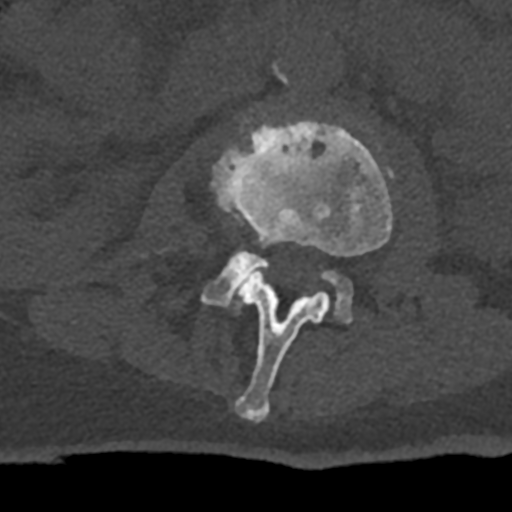
CT including the spine, one axial slice. Slice 357 of 797 in the series (ordered by position). Reconstruction kernel Br40s/3. Bone window (W 1800 / L 400 HU). 0.5 mm slice thickness. 512 × 512 image matrix, field of view 160 × 160 mm. Male patient, age 74 years. Case-level facts recorded for this patient, not image findings: primary cancer: renal.
Structures marked on this image (semi-automatic segmentation, software-assisted and operator-edited):
- L2 vertebra: bounding box (x1, y1, x2, y2) in pixels: (211, 119, 393, 421)
- L3 vertebra: (202, 251, 352, 322)